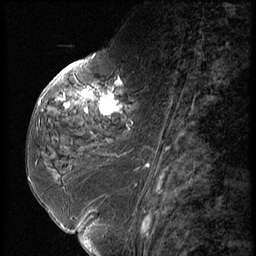
Breast MRI (dynamic contrast-enhanced), one sagittal slice; dynamic contrast-enhanced series, image 2 of 3 at this slice position (ordered by acquisition); 1.5 T; TE 4.2 ms, TR 9 ms; 256 × 256 image matrix, field of view 180 × 180 mm. Female patient, age 59 years. Case-level facts recorded for this patient, not image findings: setting: breast cancer imaged before/during neoadjuvant chemotherapy; receptor status: HER2-positive.
Outlined on this slice (semi-automatic segmentation, software-assisted and operator-edited):
- analysis volume of interest (the breast-tissue region the enhancement analysis was run in; not a lesion): box from (x=44, y=66) to (x=151, y=135) px
- tumour enhancement mask (voxels above the 140 % enhancement threshold inside the analysis volume of interest): (x=64, y=78)–(x=122, y=115)